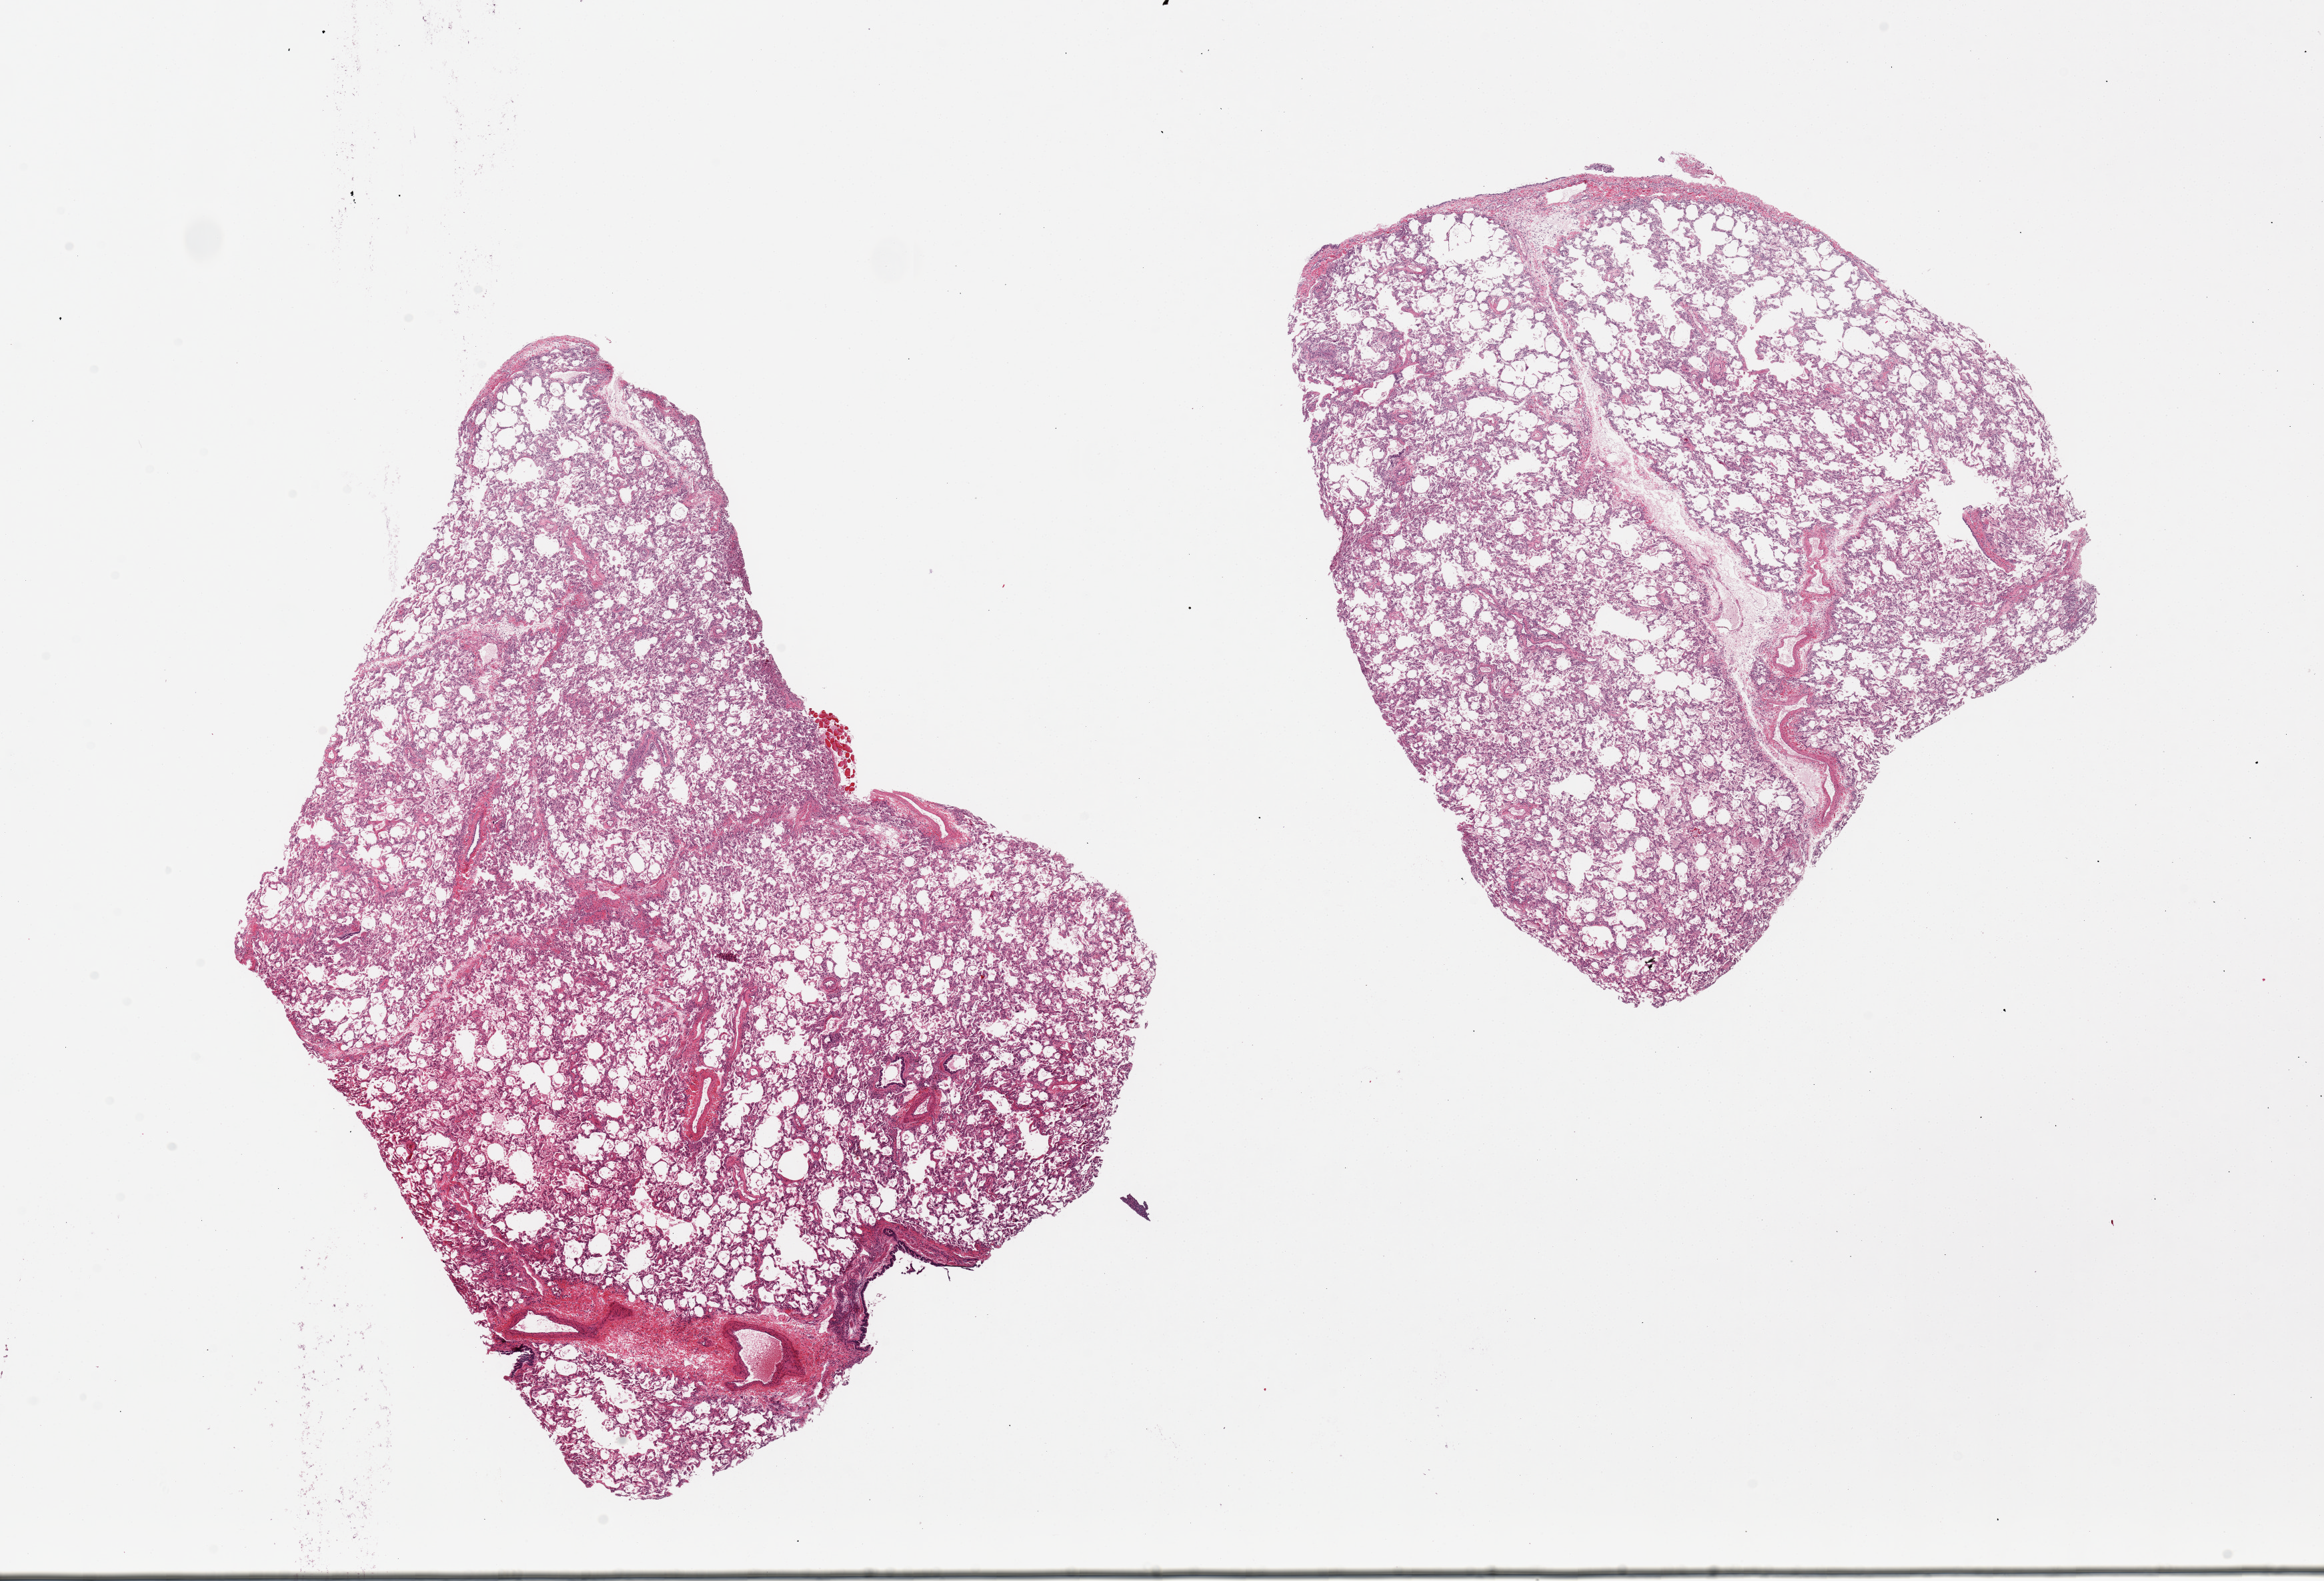
Haematoxylin and eosin whole-slide image — a low-resolution overview of the entire scanned area, about 27.6 x 18.8 mm (from a 20x scan); PAXgene-fixed paraffin-embedded (PFPE) section; target tissue: lung; donor tissue sample.
Pathologist's review note for this sample: 2 pieces. 12x9 & 10x9mm.